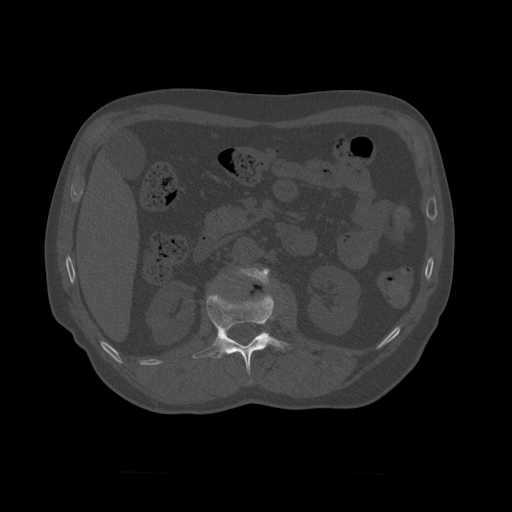
CT including the spine, one axial slice. Slice 351 of 450 in the series (ordered by position). 120 kVp. Bone window (W 1800 / L 400 HU). 1.25 mm slice thickness. 512 × 512 image matrix. Patient age 75 years. From the clinical record (not read from this slice): primary cancer: prostate.
Structures marked on this image (semi-automatic segmentation, software-assisted and operator-edited):
- L1 vertebra: bounding box (x1, y1, x2, y2) in pixels: (192, 291, 292, 384)
- L2 vertebra: (237, 268, 271, 290)